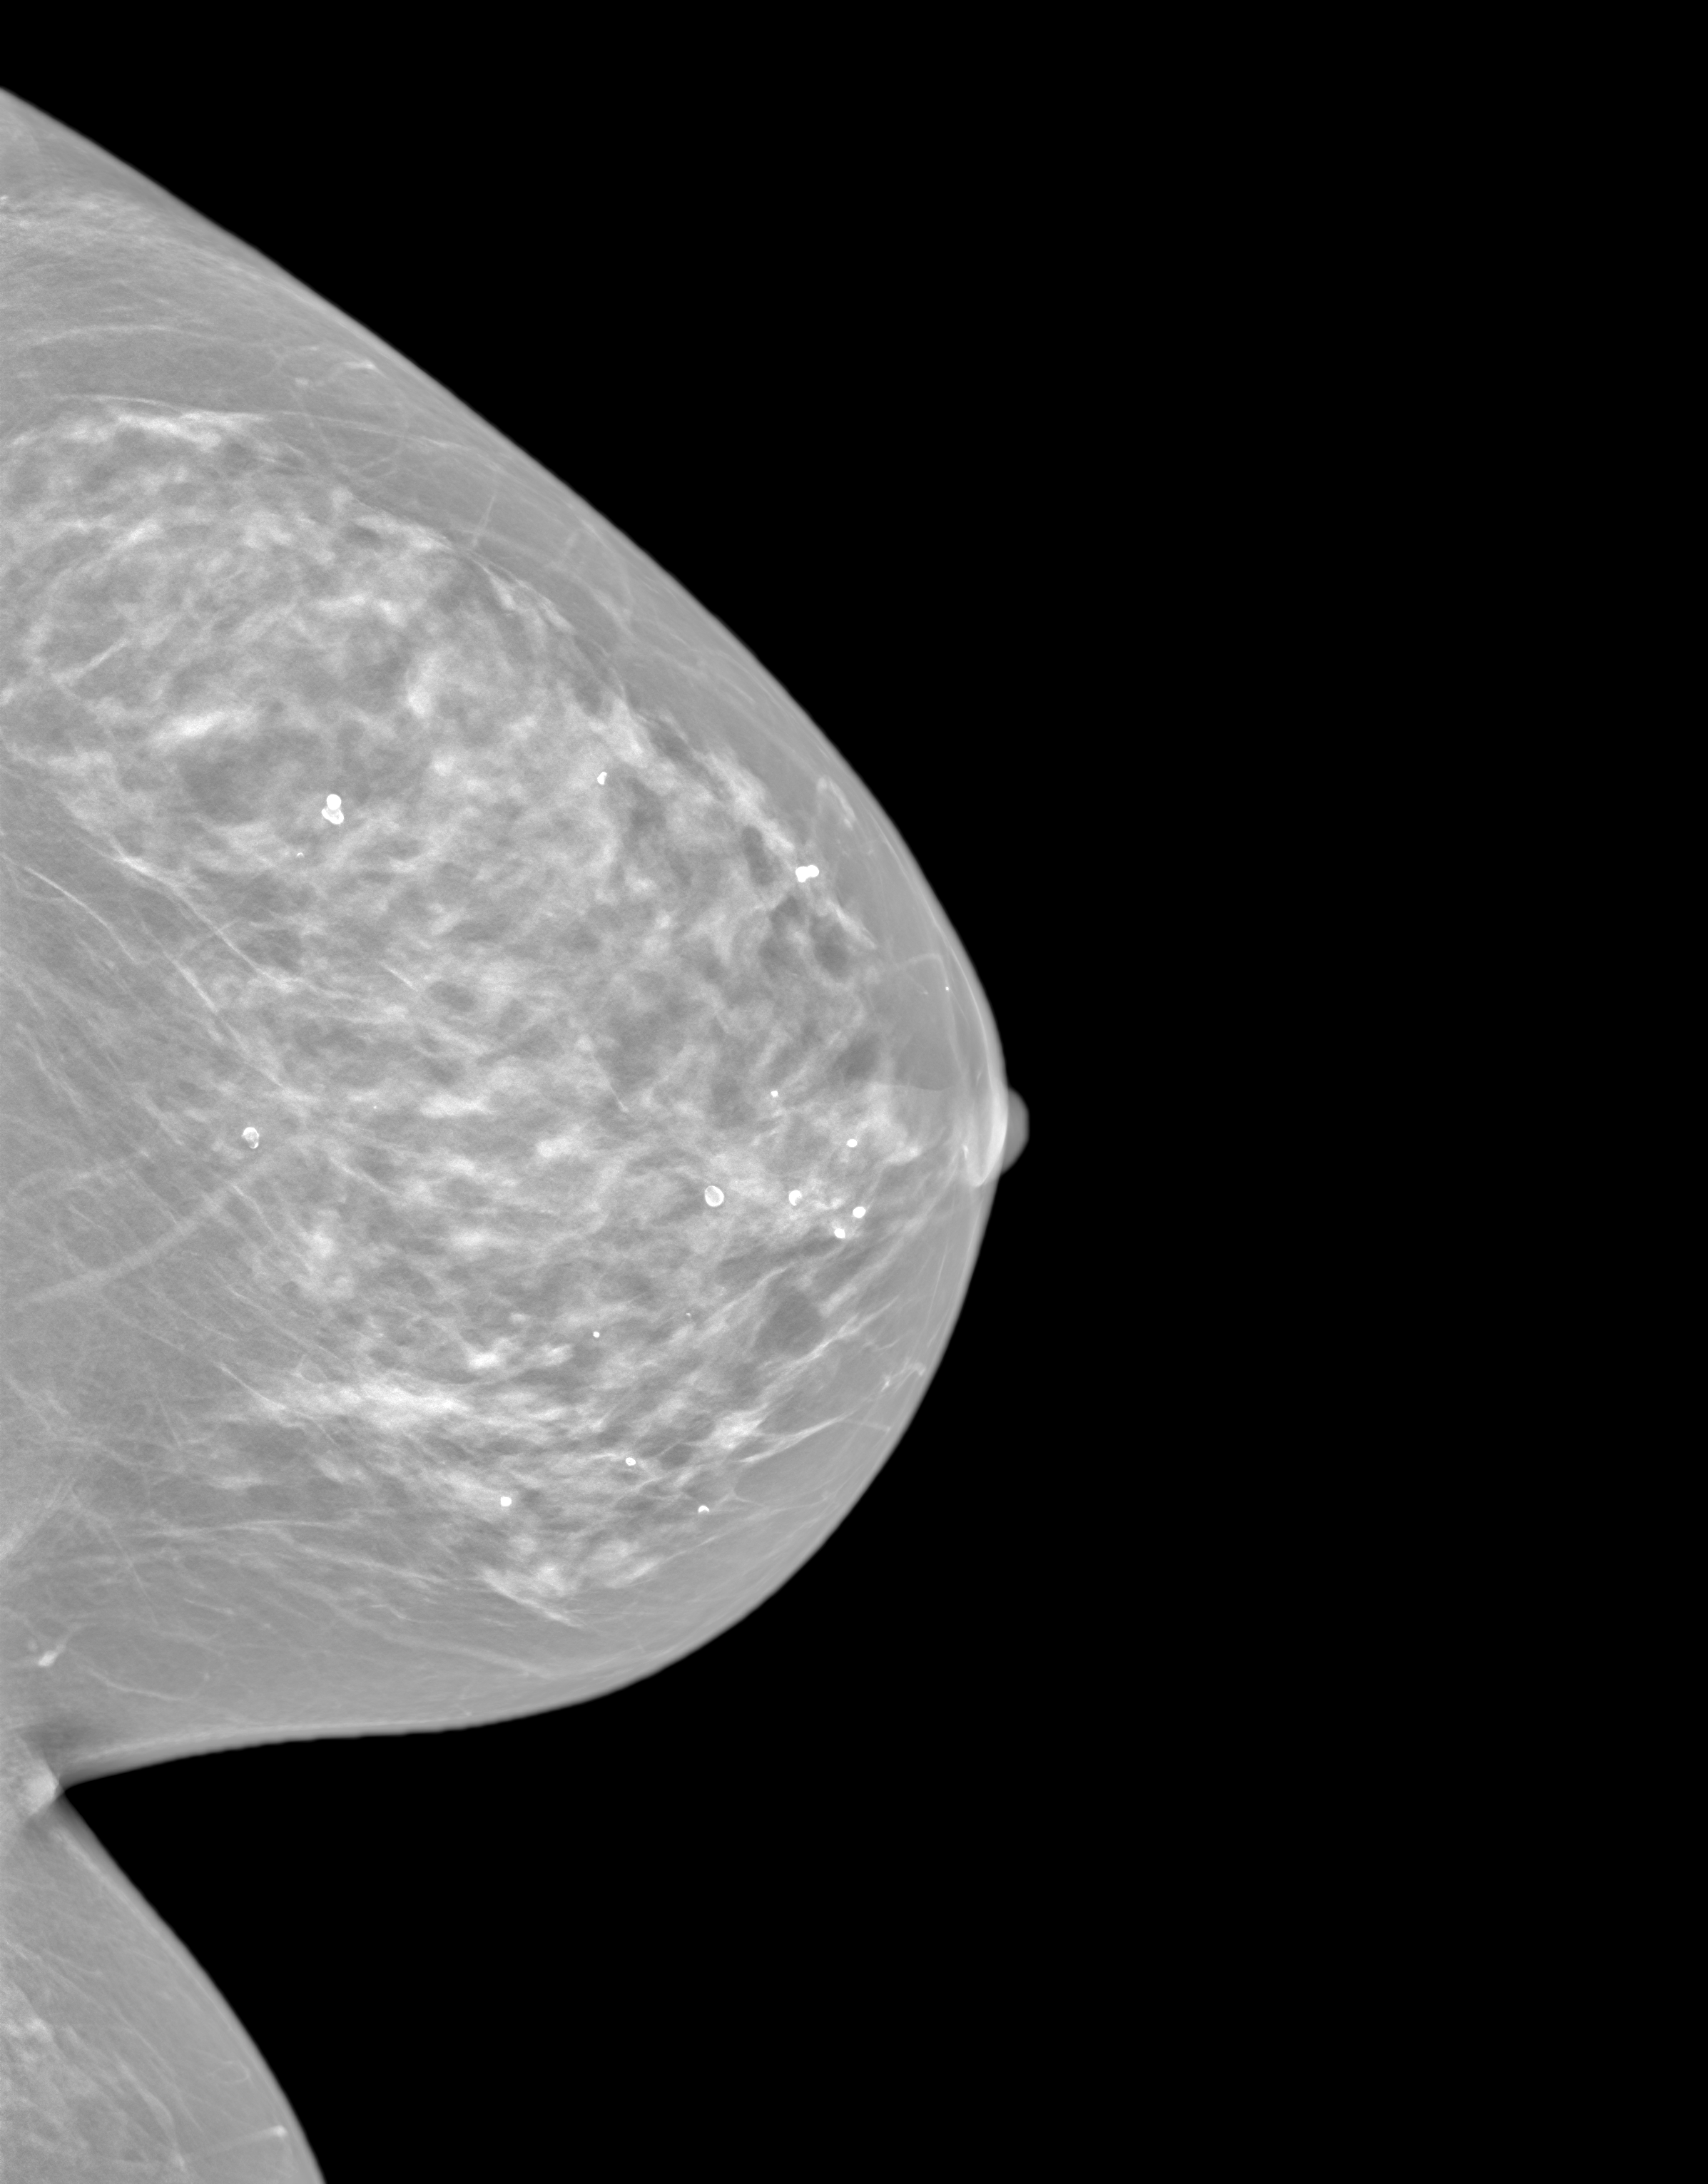
Synthetic 2-D view generated from a tomosynthesis acquisition (not an FFDM exposure); left breast; craniocaudal (CC) view; screening examination. Female patient, age 66 years.
- BI-RADS breast density category at the screening exam (both breasts, scale 1–4): 3
- final BI-RADS category for the screening round (tomosynthesis exam, both breasts): category 1
- recall: no recall after this screen